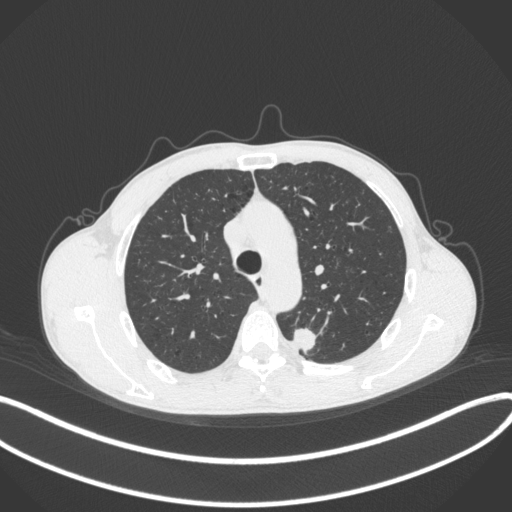
Chest CT, one axial slice. Slice 289 of 429 in the series (ordered by position). 120 kVp. Lung window (W 1500 / L -600 HU). 1 mm slice thickness. 512 × 512 image matrix, field of view 400 × 400 mm. Patient: male, 51 years. From the clinical record (not read from this slice): clinical TNM (as recorded): T2a N1 M1.
Annotated regions visible in this slice (bounding box drawn by a radiologist):
- lung tumour (recorded histology: adenocarcinoma): bounding box [x1, y1, x2, y2] px = [288, 321, 319, 357]